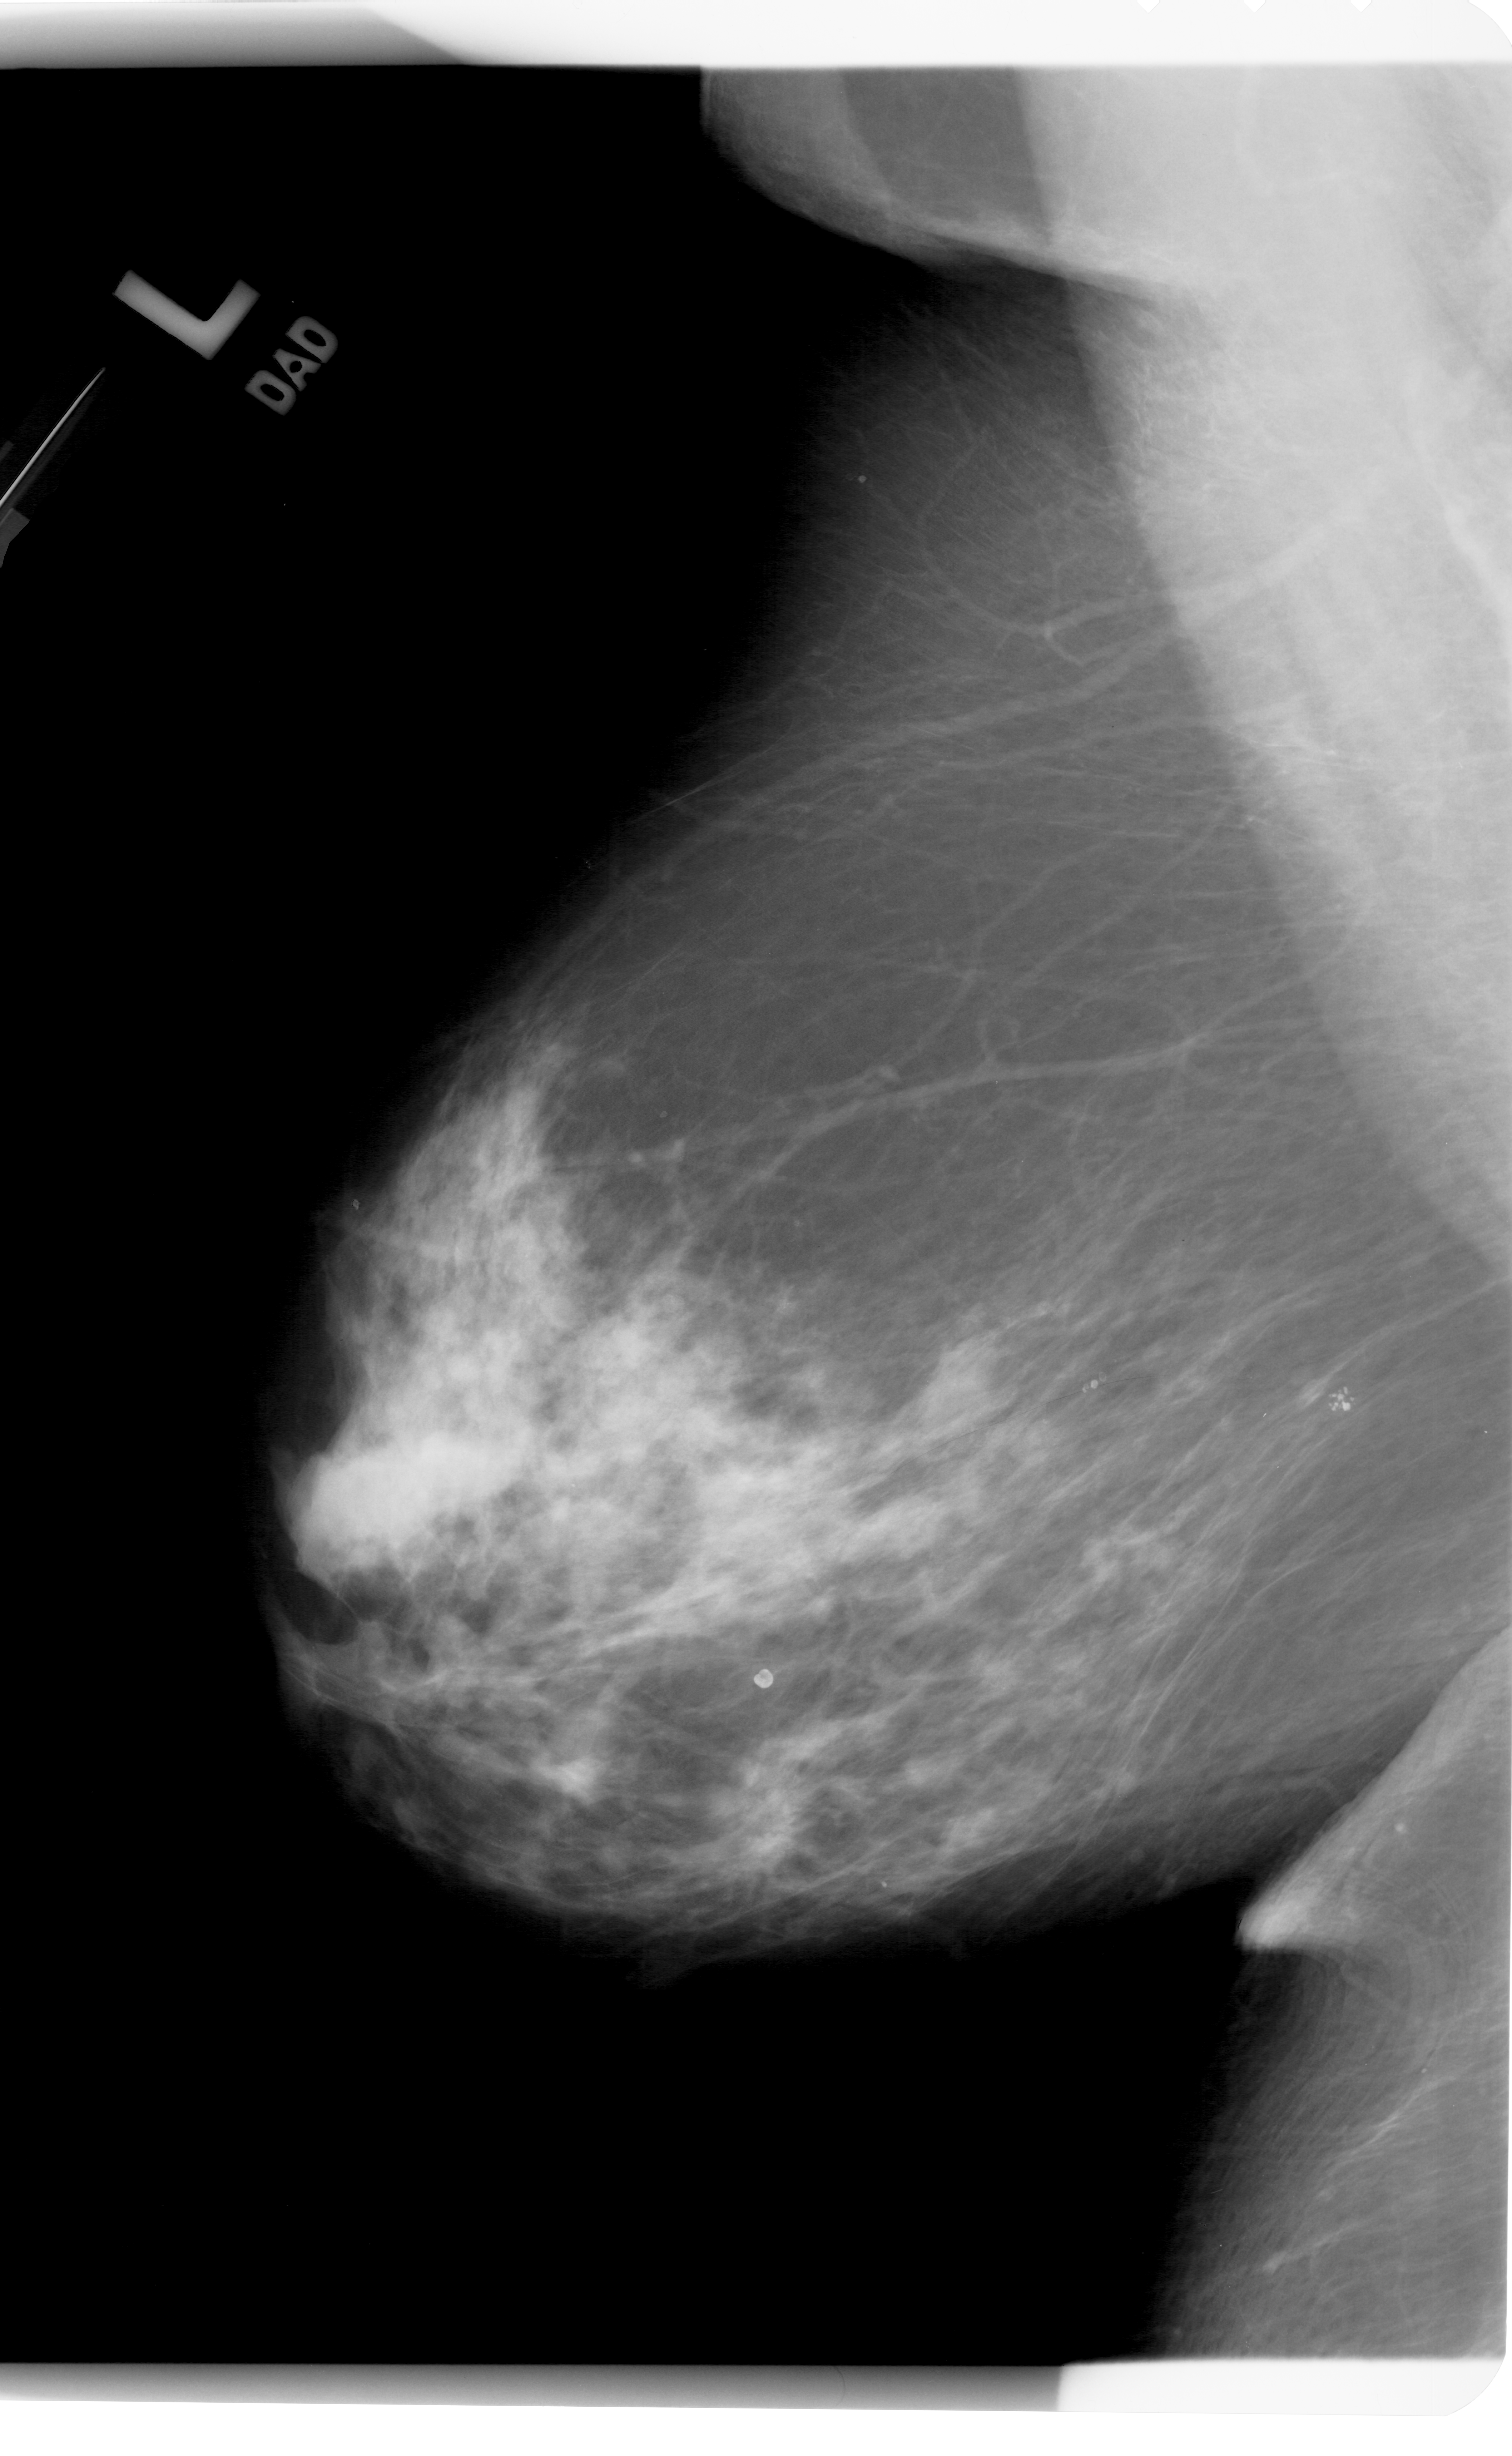
Digitized screen-film mammogram; left breast; mediolateral oblique (MLO) view; breast composition: heterogeneously dense (BI-RADS density category 3 of 4).
Finding: mass, shape architectural distortion, margins spiculated; BI-RADS assessment category 5; subtlety rating 2 on a 1 (subtle) to 5 (obvious) scale; pathology (as recorded): malignant.